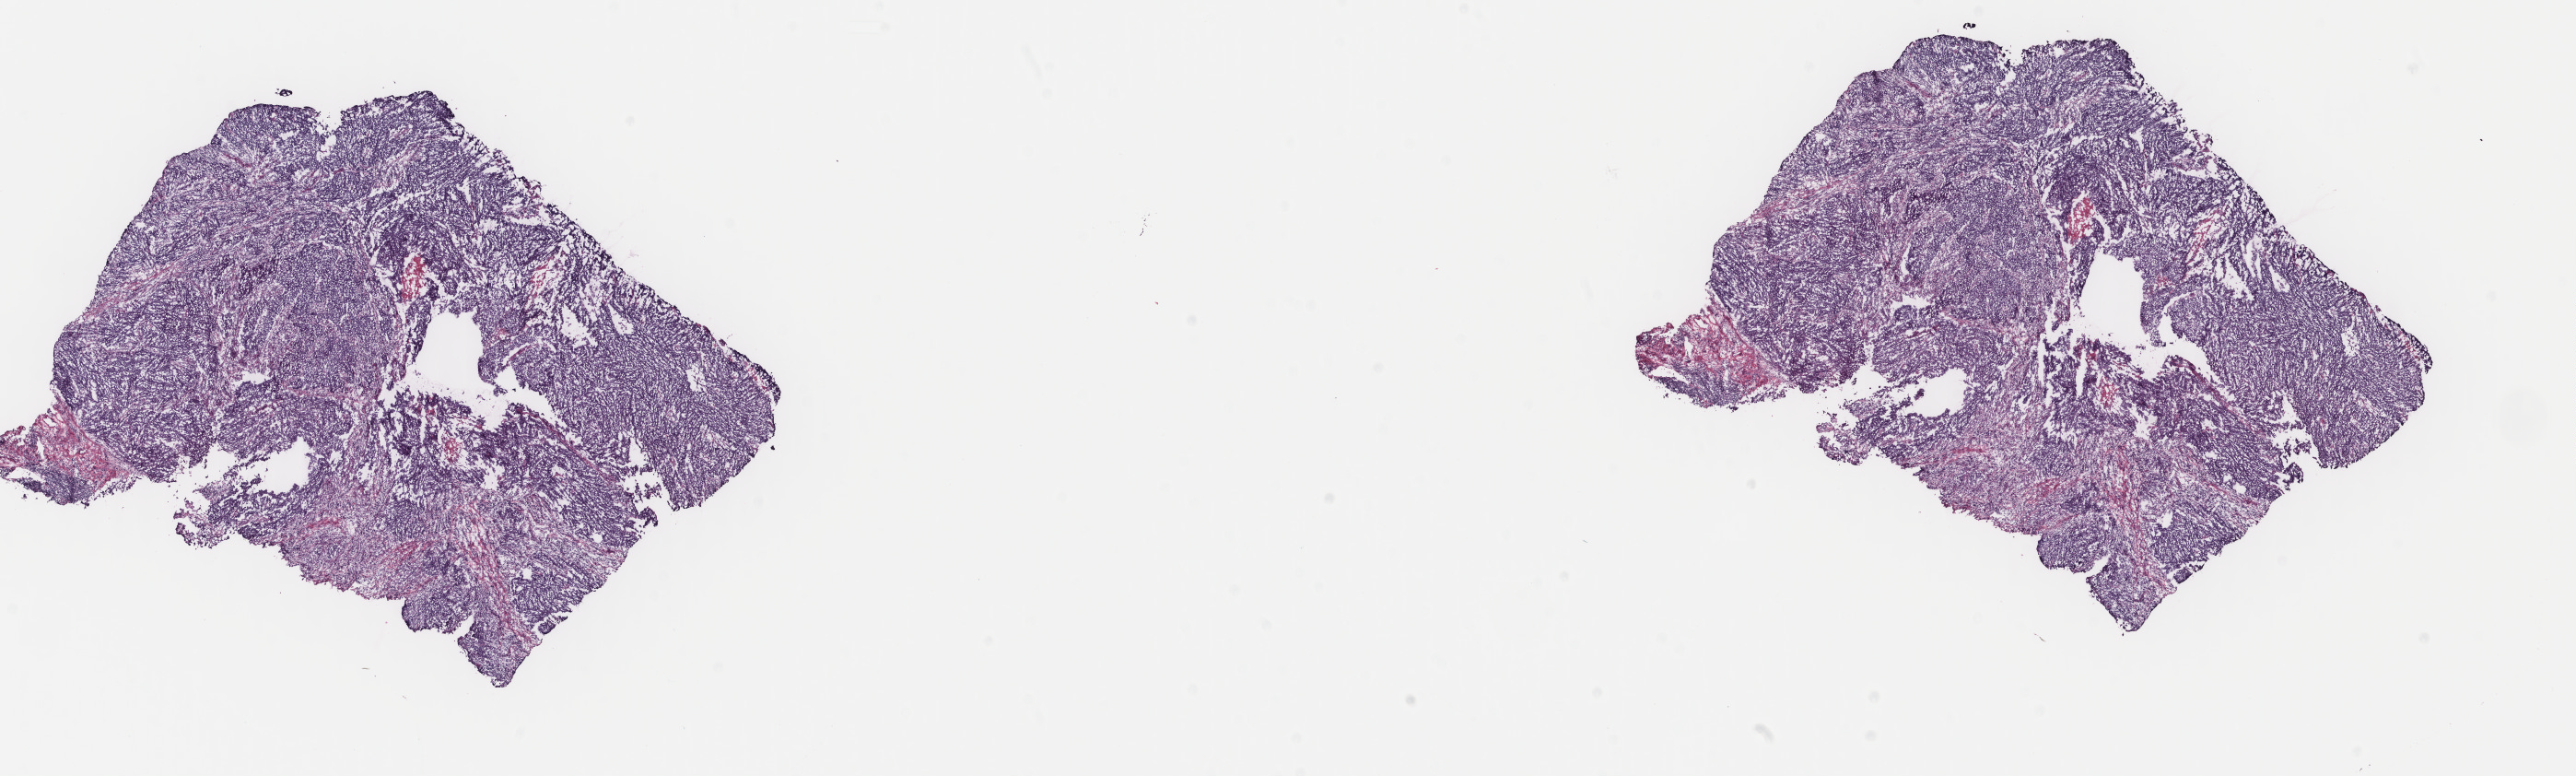
H&E whole-slide image — a low-resolution overview of the entire scanned area, about 22.2 x 6.7 mm, frozen section from the top of the tissue portion, uterus, primary tumour sample. Female patient. Histologic grade: G3 (poorly differentiated). Composition of this section per pathologist review: tumour cells 90%, tumour nuclei 90%, normal cells 0%, stromal cells 10%, necrosis 0%. Infiltration values recorded for this section: lymphocyte infiltration 15%, monocyte infiltration 3%, neutrophil infiltration 3%.
FIGO stage: IB. Pathologic diagnosis: Endometrioid adenocarcinoma, NOS.